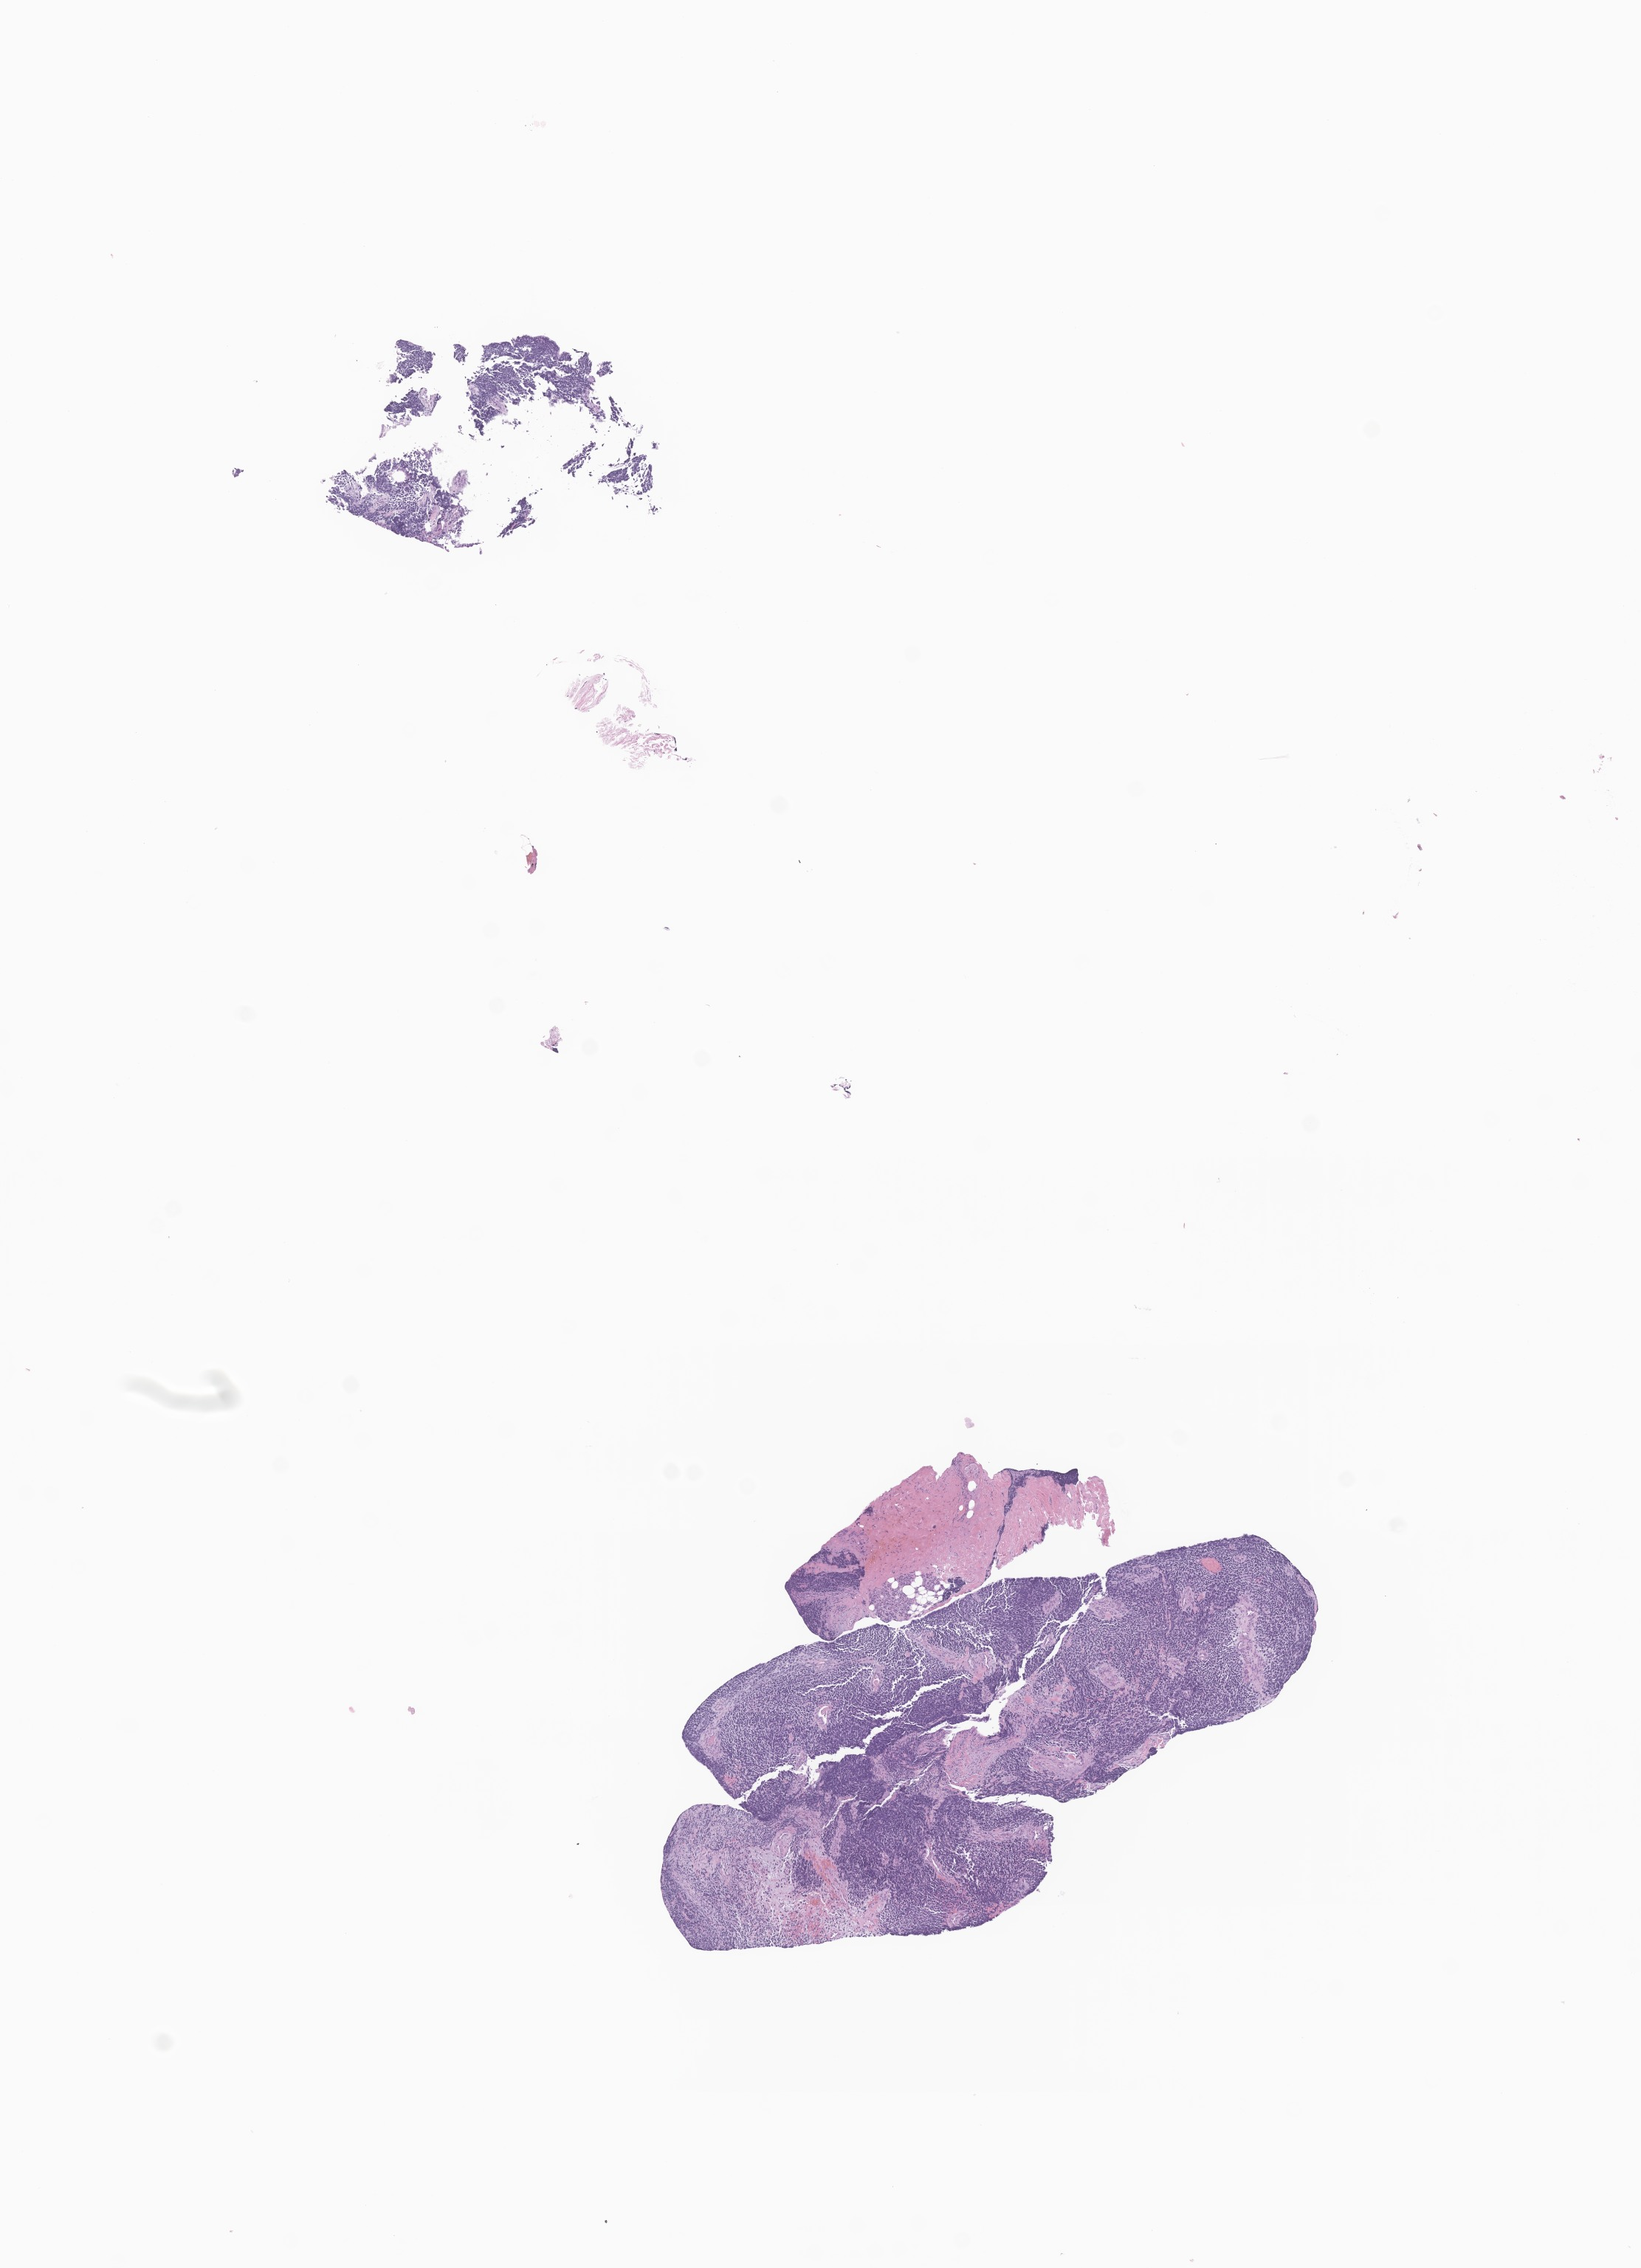
Digitized haematoxylin and eosin-stained section of tumor tissue from the parotid gland, a low-resolution overview of the entire scanned area, about 9.4 x 13.0 mm. Formalin-fixed, paraffin-embedded (FFPE) tissue. Patient male; age 140 months.
Recorded diagnosis: Embryonal rhabdomyosarcoma, NOS.